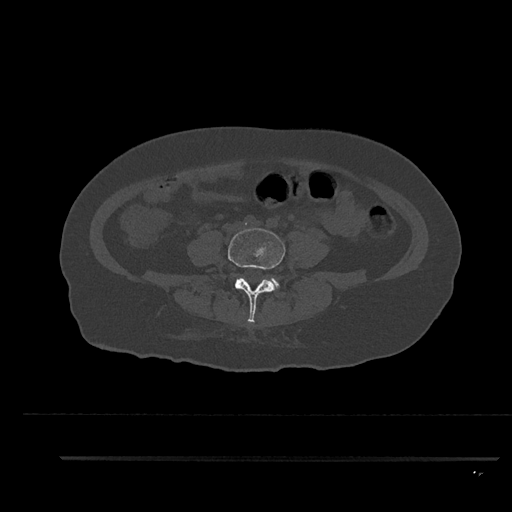
CT including the spine, one axial slice; position 7 of 797 along the scan axis; bone window (W 1800 / L 400 HU); 0.5 mm slice thickness; 512 × 512 image matrix, field of view 408 × 408 mm. Patient: female, 44 years. From the clinical record (not read from this slice): primary cancer: renal; vertebrae with lytic lesions (as recorded): L1.
Outlined on this slice (semi-automatically segmented with operator editing):
- L4 vertebra: bounding box (x1, y1, x2, y2) in pixels: (228, 228, 286, 323)